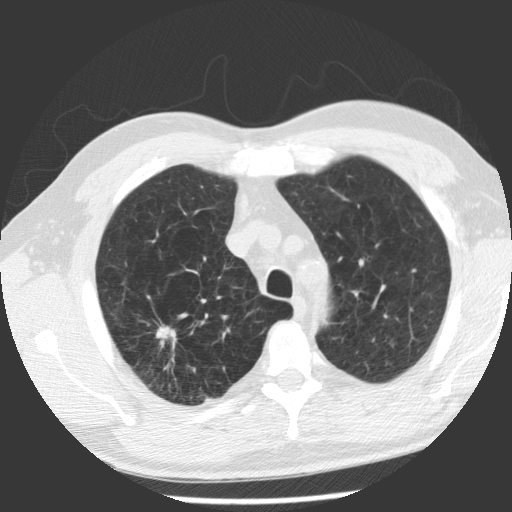
Chest CT (low-dose screening protocol), one axial image. Baseline screening round. Lung window (W 1500 / L -600 HU). 2.5 mm slice thickness. Standard (soft-tissue) reconstruction kernel (STANDARD). 140 kVp. Slice 88 of 112 in the series. 512 × 512 image matrix. Male participant, aged 62 years at enrolment. Former smoker at enrolment.
- Lesion marked by an expert reader, box from (x=119, y=302) to (x=198, y=382) px.
- The screening reader recorded 2 non-calcified nodules or masses ≥4 mm on this exam; which of them this box marks is not recorded.
- Official screen result: positive, change unspecified: nodule(s) >= 4 mm or enlarging nodule(s), mass(es), or other non-specific abnormalities suspicious for lung cancer.
- Participant outcome: lung cancer diagnosed 71 days after this screen — adenocarcinoma, NOS, right upper lobe, poorly differentiated (G3), stage IV (AJCC 6th edition), 30 mm at pathology.